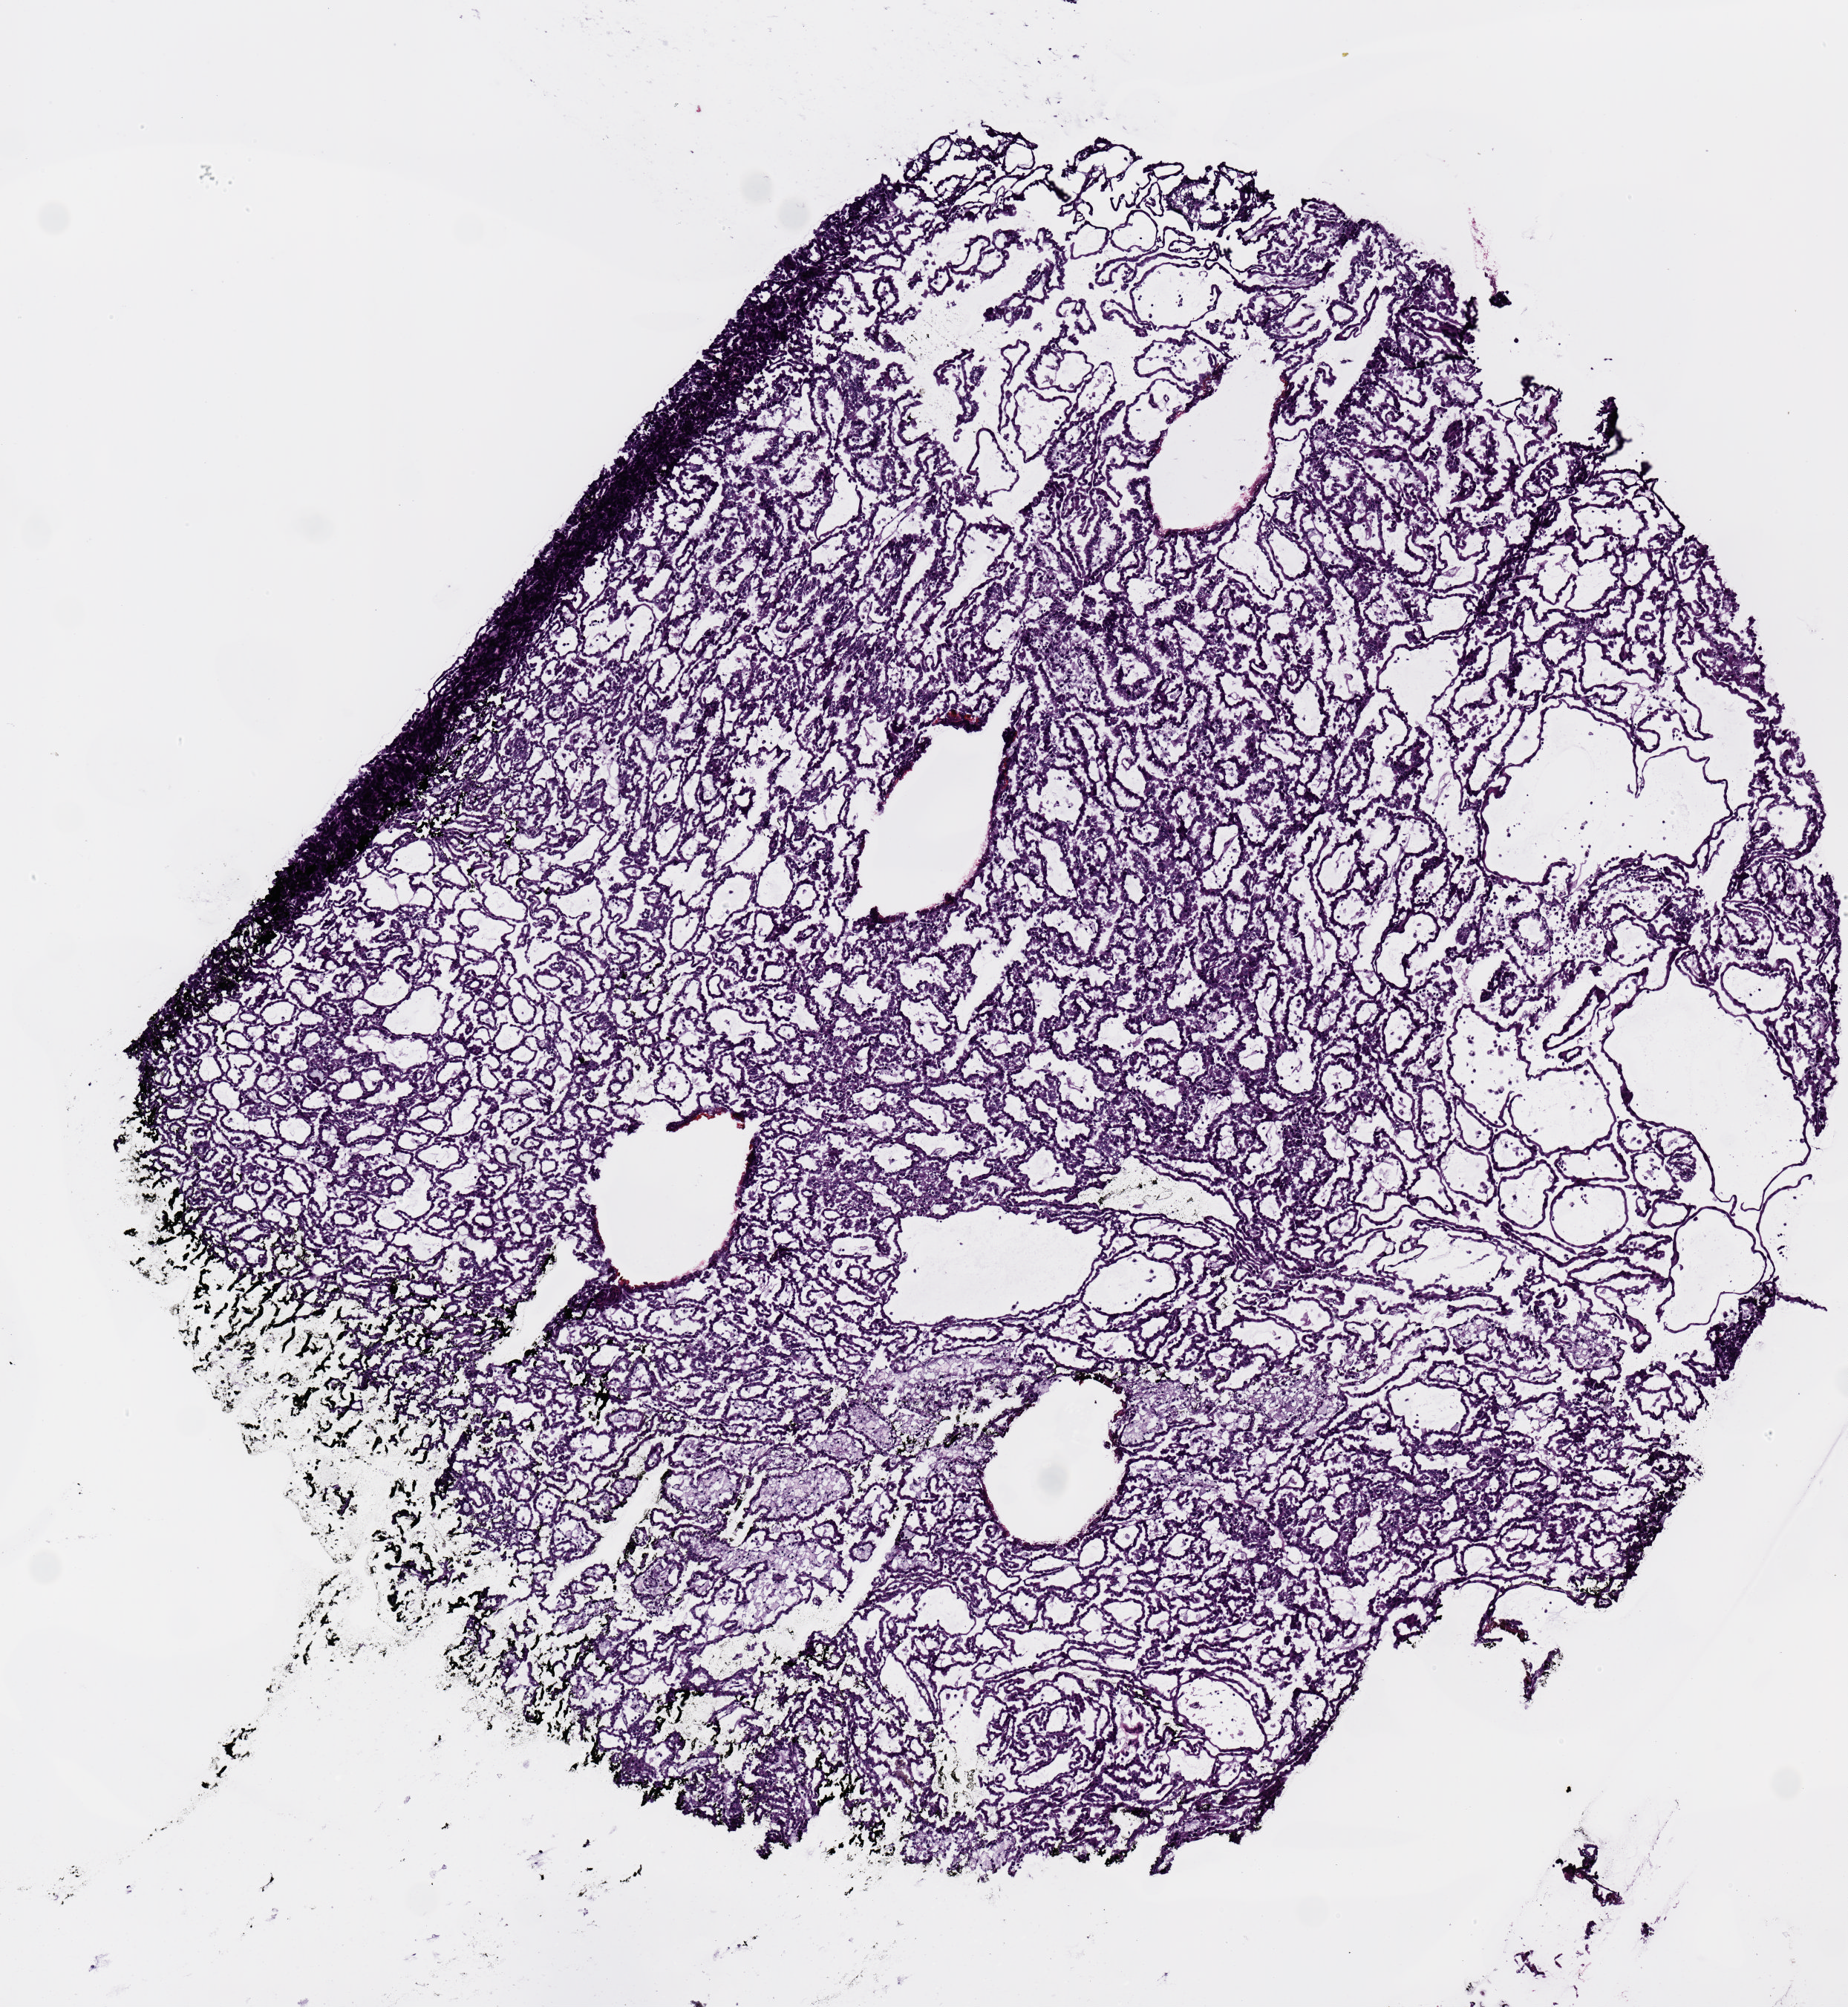
Digitized H&E tissue section (whole slide) — shown as a low-resolution overview of the whole scanned area (about 4.9 x 5.3 mm); frozen section; primary tumour sample from the kidney. Male patient; age at initial diagnosis 62 years. Composition of this section per pathologist review: tumour nuclei 90%, necrosis 0%.
Diagnosis: Papillary adenocarcinoma, NOS.